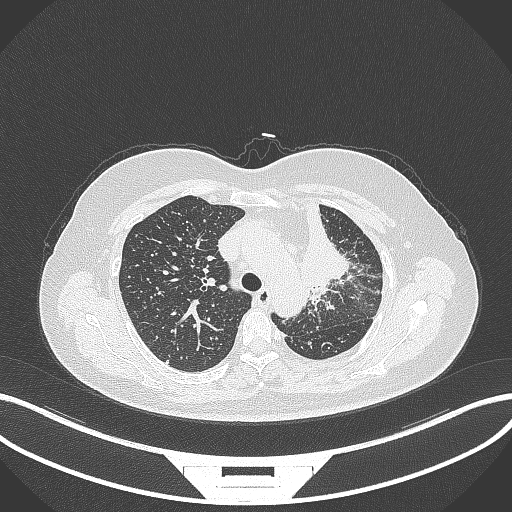
Chest CT, one axial slice; position 244 of 348 along the scan axis; reconstruction kernel B70f; 120 kVp; lung window (W 1500 / L -600 HU); 512 × 512 image matrix, field of view 400 × 400 mm. Female patient, age 49 years. From the clinical record (not read from this slice): clinical TNM (as recorded): T1c N0 M1.
Outlined on this slice (bounding box drawn by a radiologist):
- lung tumour (recorded histology: adenocarcinoma): bounding box <295,196,353,307> (left, top, right, bottom; pixels)